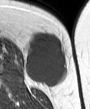
MRI of an extremity soft-tissue mass, one axial slice. Position 14 of 45 along the scan axis. MR volume resampled by the dataset authors to the PET/CT grid (not the native acquisition matrix). 3.27 mm slice thickness. 90 × 109 image matrix, field of view 88 × 106 mm. Female patient. Case-level facts recorded for this patient, not image findings: histological type: leiomyosarcoma; grade: intermediate; site of the primary tumour: parascapusular.
Annotated regions visible in this slice (expert contour drawn on MRI and transferred to this co-registered scan by the dataset authors):
- gross tumour volume including surrounding oedema: bounding box <26,32,66,88> (left, top, right, bottom; pixels)
- gross tumour volume (mass): <26,32,66,86>